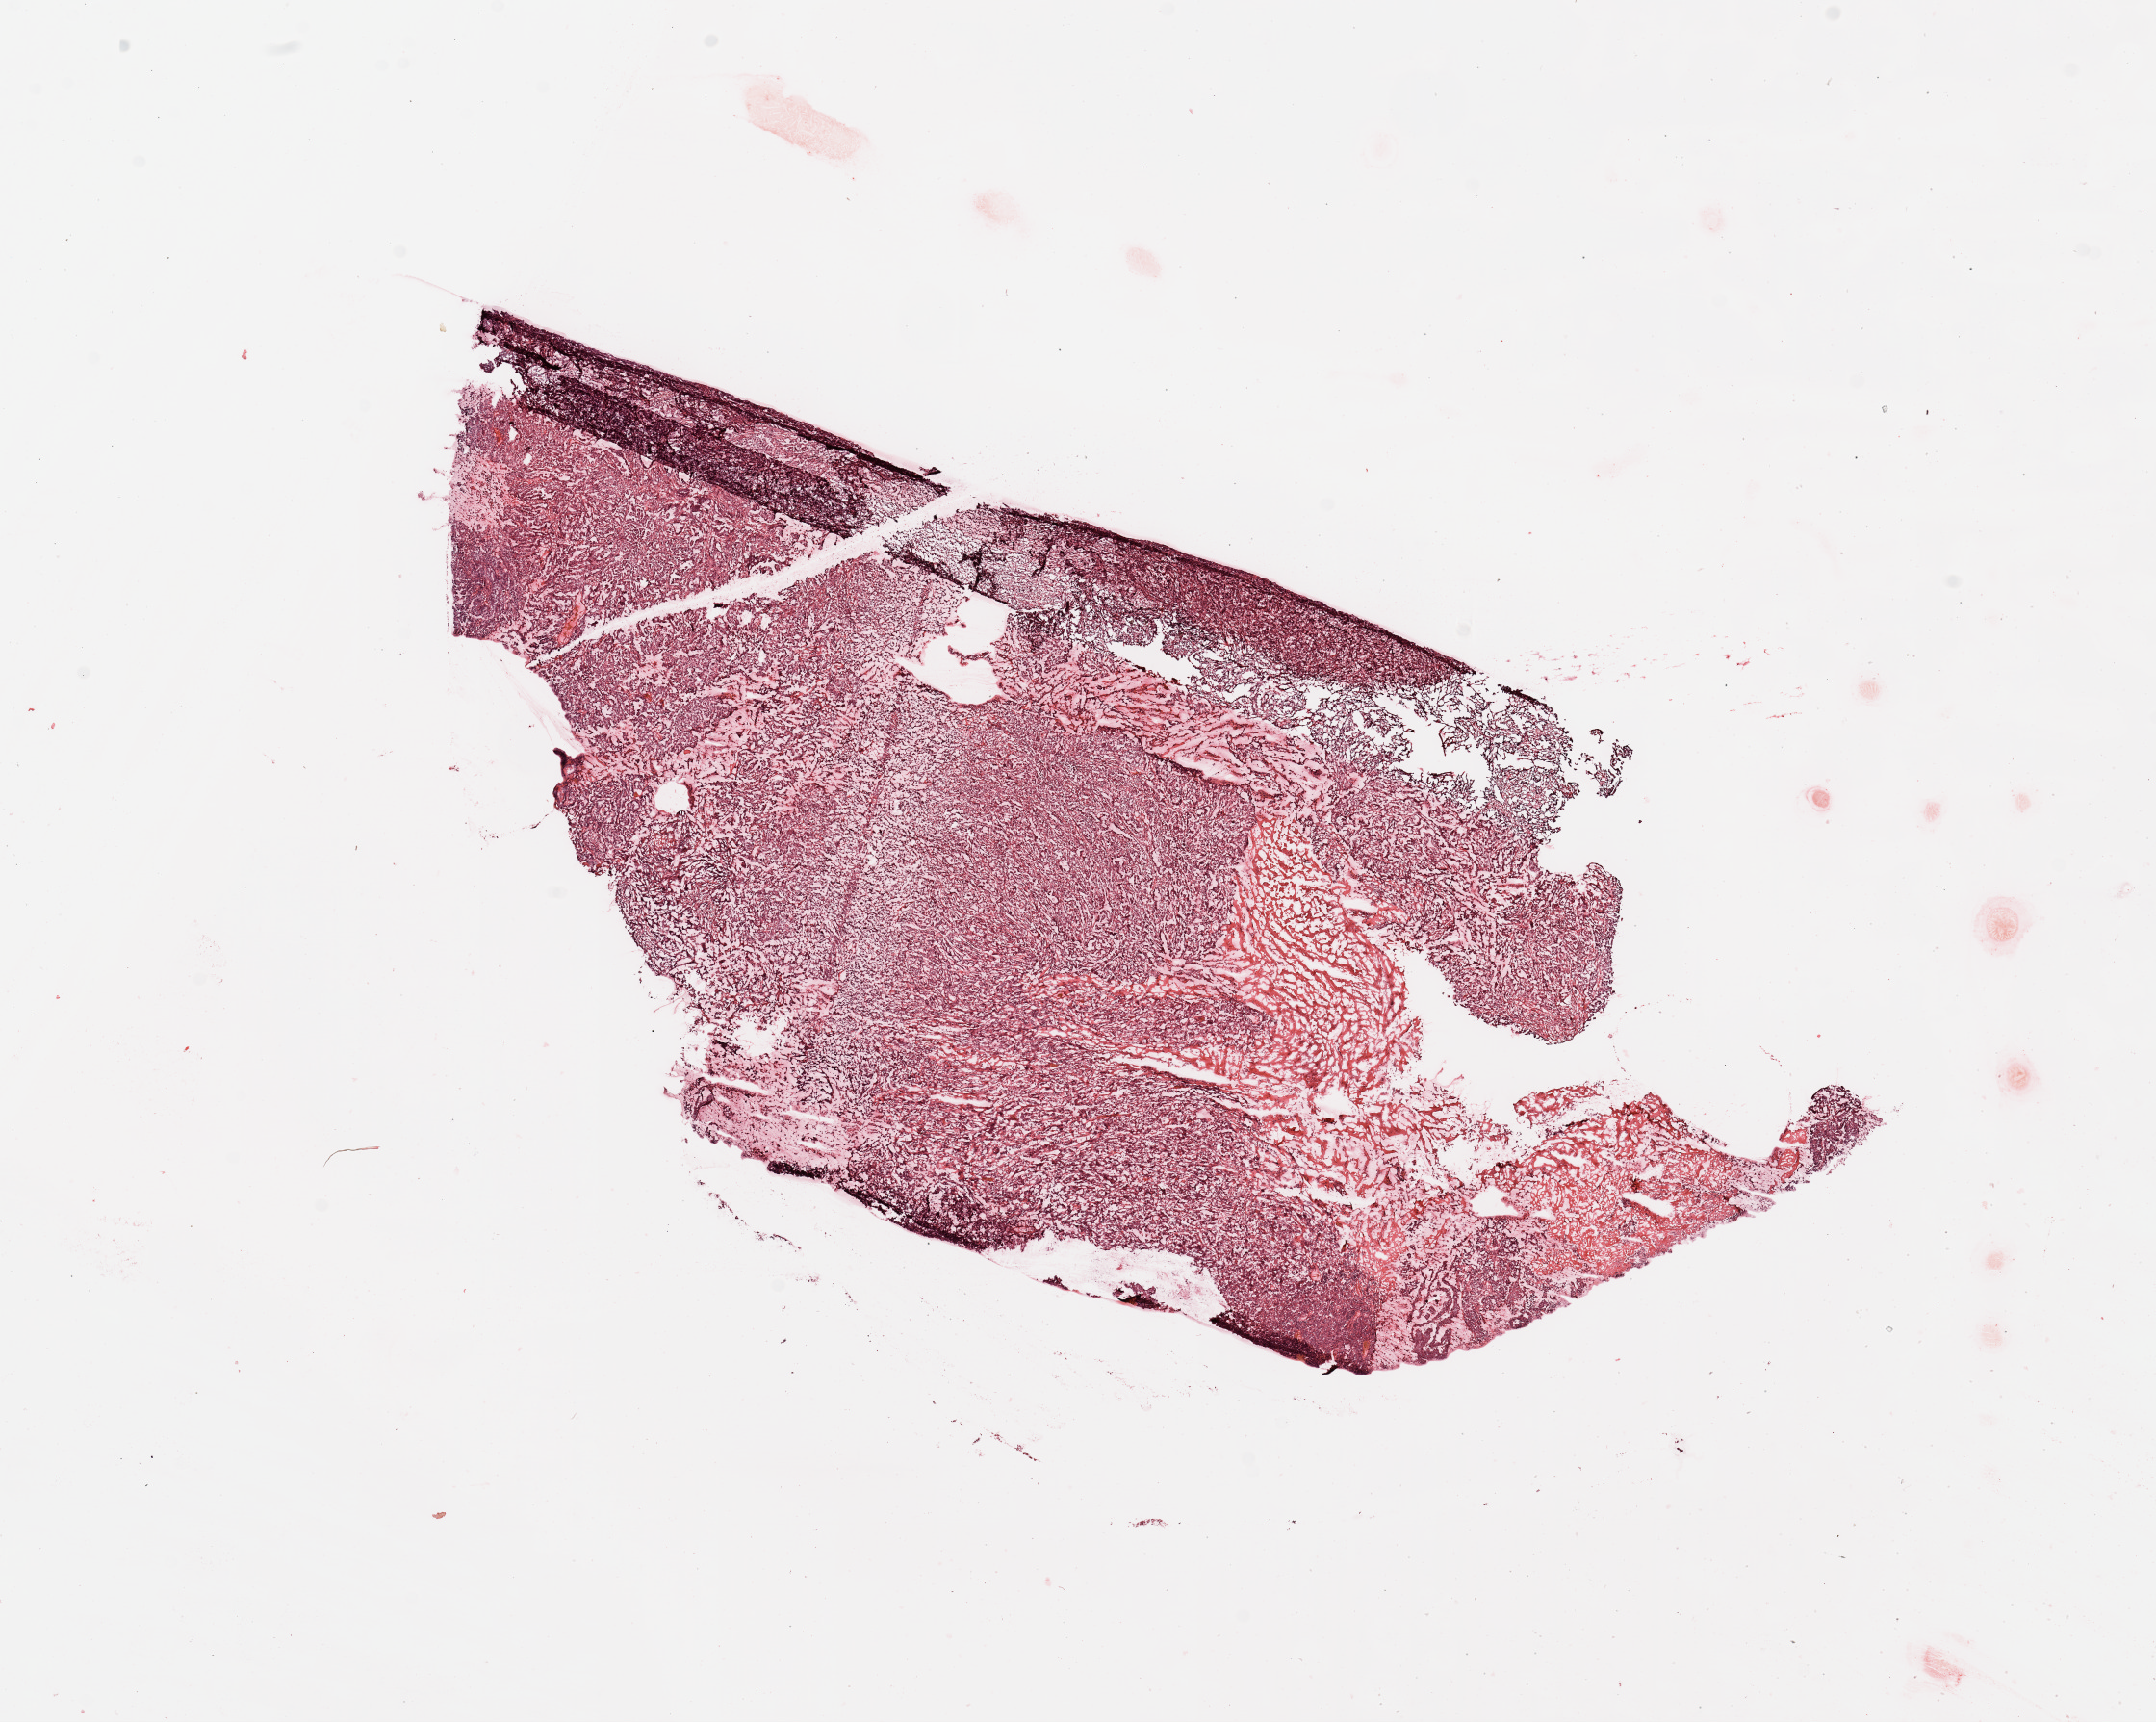
Whole-slide histology image, H&E, a low-resolution overview of the entire scanned area, about 17.7 x 14.2 mm (slide scanned at 20x), tumour tissue sample, uterus. Patient: female, age 57 years. Histologic grade: G3 (poorly differentiated).
AJCC pathologic stage: I. Histologic diagnosis: Endometrioid adenocarcinoma, NOS.